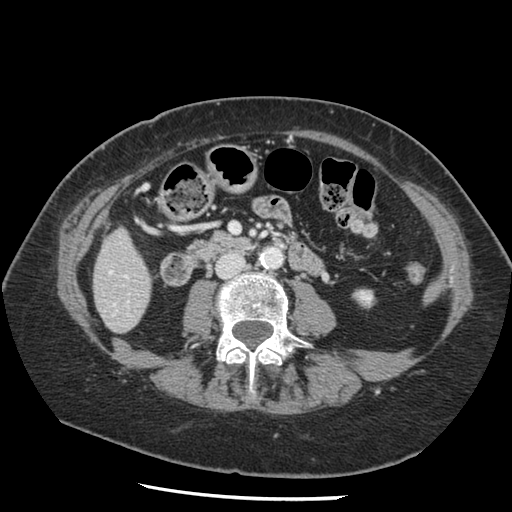
Contrast-enhanced abdominal CT, one axial slice; position 30 of 148 along the scan axis; 120 kVp; intravenous contrast given; soft-tissue window (W 400 / L 40 HU); 512 × 512 image matrix, field of view 330 × 330 mm. Female patient, age 85 years. Case-level facts recorded for this patient, not image findings: diagnosis: colorectal cancer liver metastases, imaged before liver resection; multiple liver metastases: no; largest metastasis: 0.9 cm.
Outlined on this slice (manually delineated by an expert):
- hepatic veins: bounding box (x1, y1, x2, y2) in pixels: (109, 271, 111, 273)
- liver: (94, 231, 151, 333)
- planned liver remnant (the part of the liver to remain after resection): (94, 231, 151, 332)